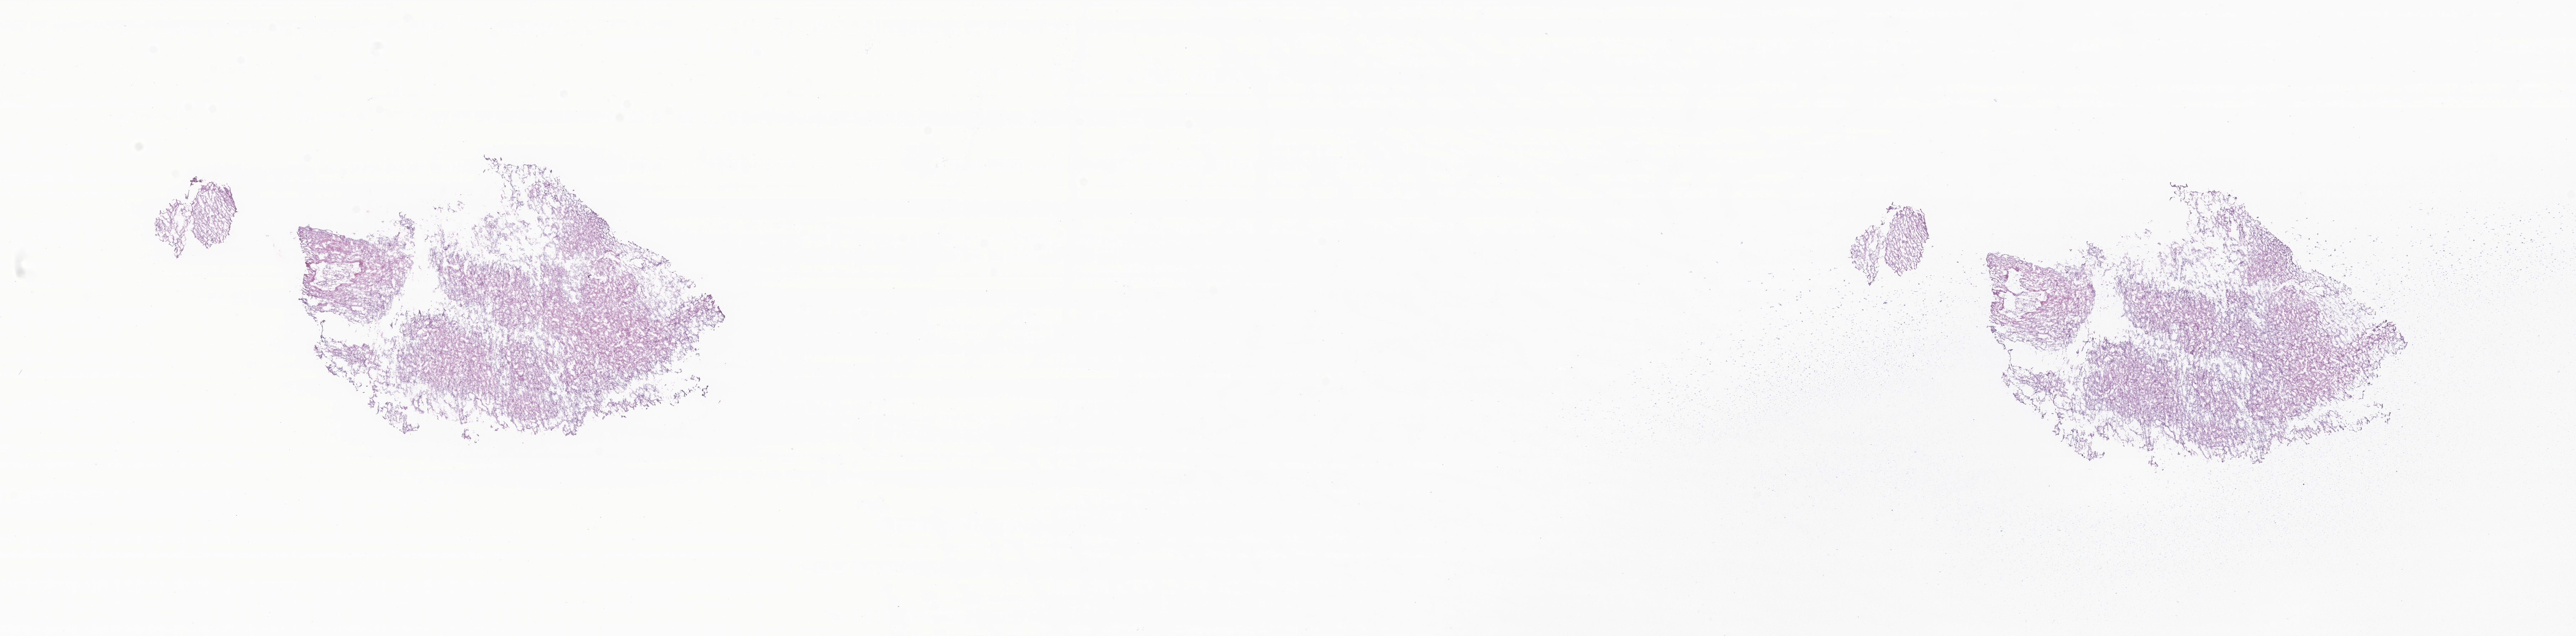
Whole-slide image, H&E stain of tumor tissue from the brain, low-resolution overview of the scanned area, about 30.5 x 7.5 mm. Frozen section (OCT-embedded). Patient male; age 44 months (3 years 8 months).
- recorded diagnosis: Pilocytic astrocytoma